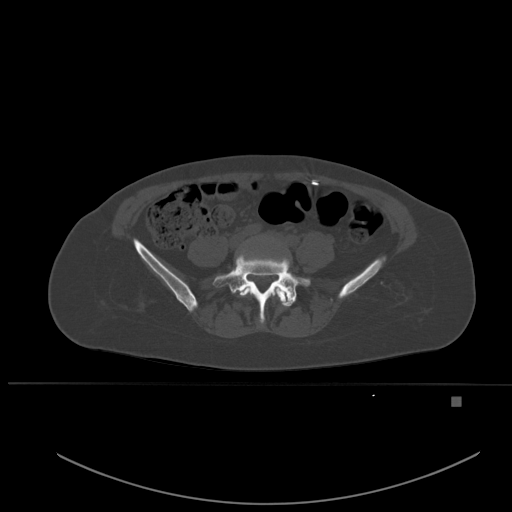
CT including the spine, one axial slice; position 159 of 651 along the scan axis; bone window (W 1800 / L 400 HU); 1.5 mm slice thickness; 512 × 512 image matrix, field of view 443 × 443 mm. Patient: female, 49 years. Case-level facts recorded for this patient, not image findings: primary cancer: breast.
Structures marked on this image (semi-automatically segmented with operator editing):
- L4 vertebra: bounding box (x1, y1, x2, y2) in pixels: (239, 286, 288, 303)
- L5 vertebra: (213, 255, 310, 323)